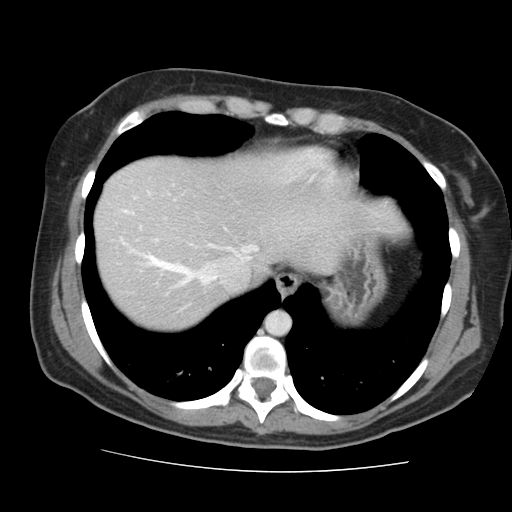
Contrast-enhanced abdominal CT, one axial slice. Position 129 of 144 along the scan axis. 120 kVp. Intravenous contrast given. Soft-tissue window (W 400 / L 40 HU). 512 × 512 image matrix, field of view 333 × 333 mm. Female patient, age 46 years. From the clinical record (not read from this slice): diagnosis: colorectal cancer liver metastases, imaged before liver resection; multiple liver metastases: no; largest metastasis: 2.8 cm.
Annotated regions visible in this slice (manually delineated by an expert):
- hepatic veins: bounding box (x1, y1, x2, y2) in pixels: (125, 211, 258, 285)
- liver: (96, 153, 342, 331)
- planned liver remnant (the part of the liver to remain after resection): (96, 153, 342, 331)
- portal vein (with intrahepatic branches): (147, 255, 176, 266)